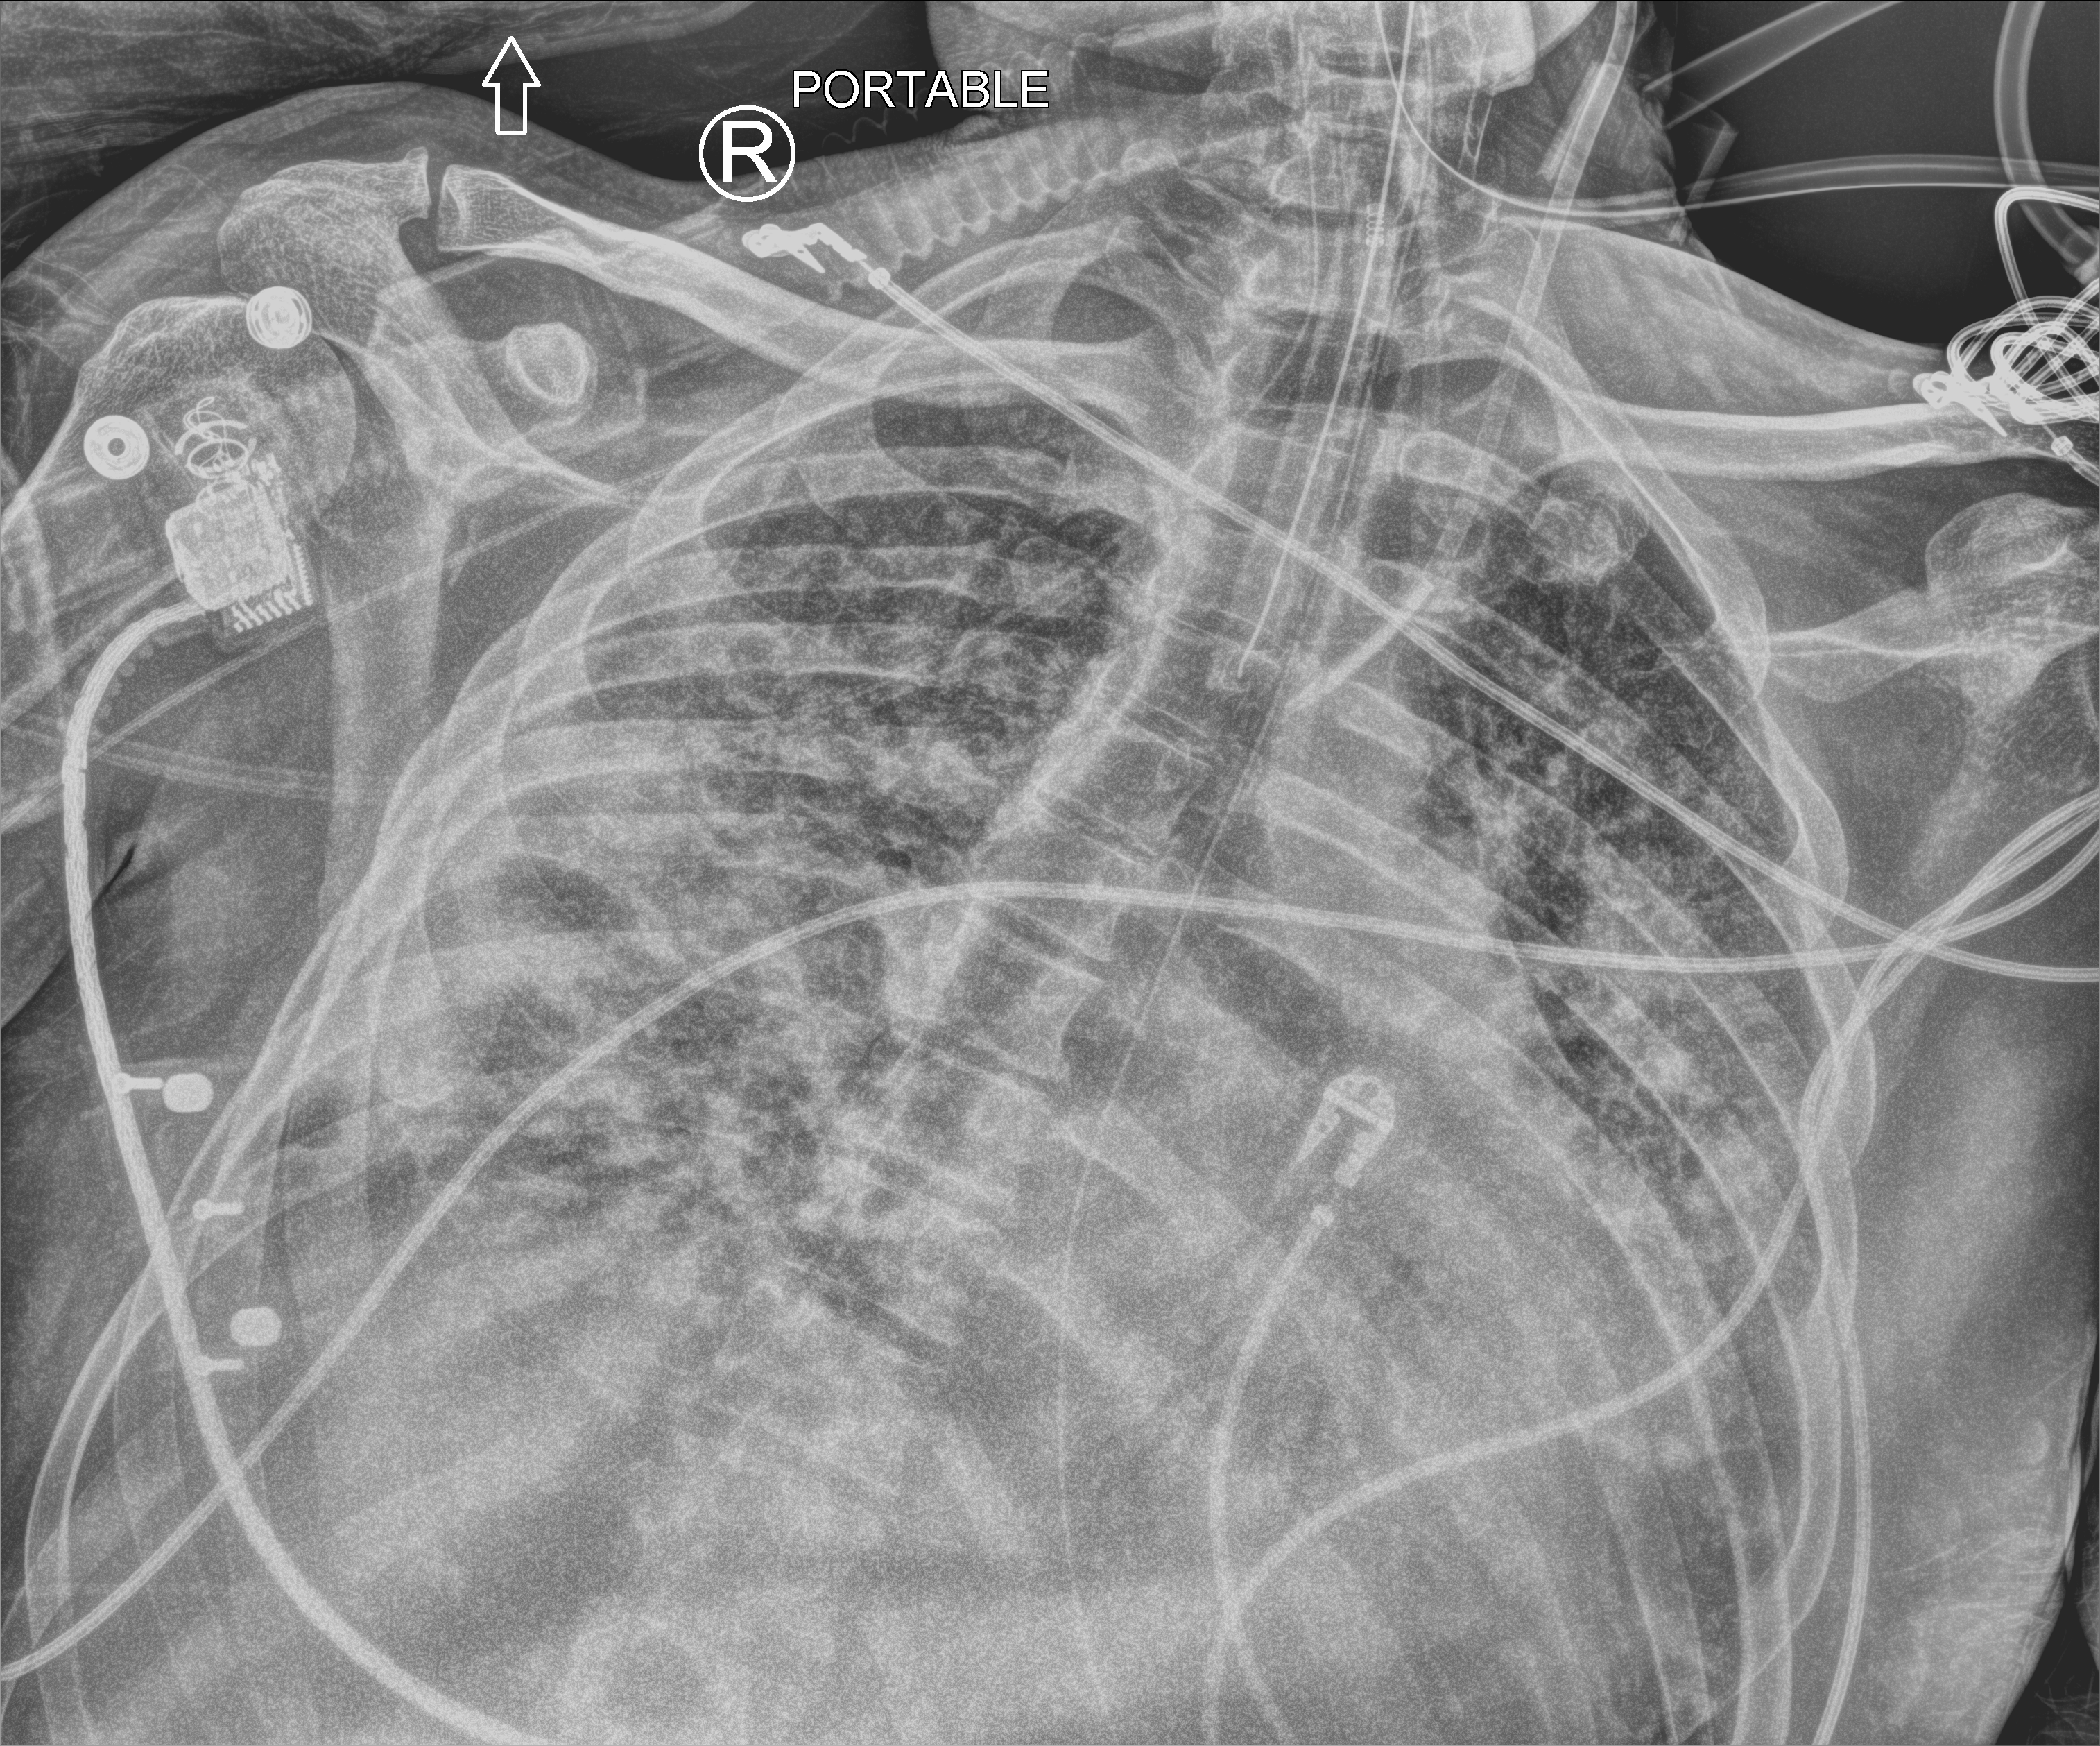
Portable chest radiograph; anteroposterior (AP) projection. Patient hospitalised with COVID-19; male, aged 18–59 years.
Admission-level facts for this patient (not findings on this image; timing relative to this image not recorded): diabetes (admission record): no; admitted to intensive care during this hospital stay: yes.